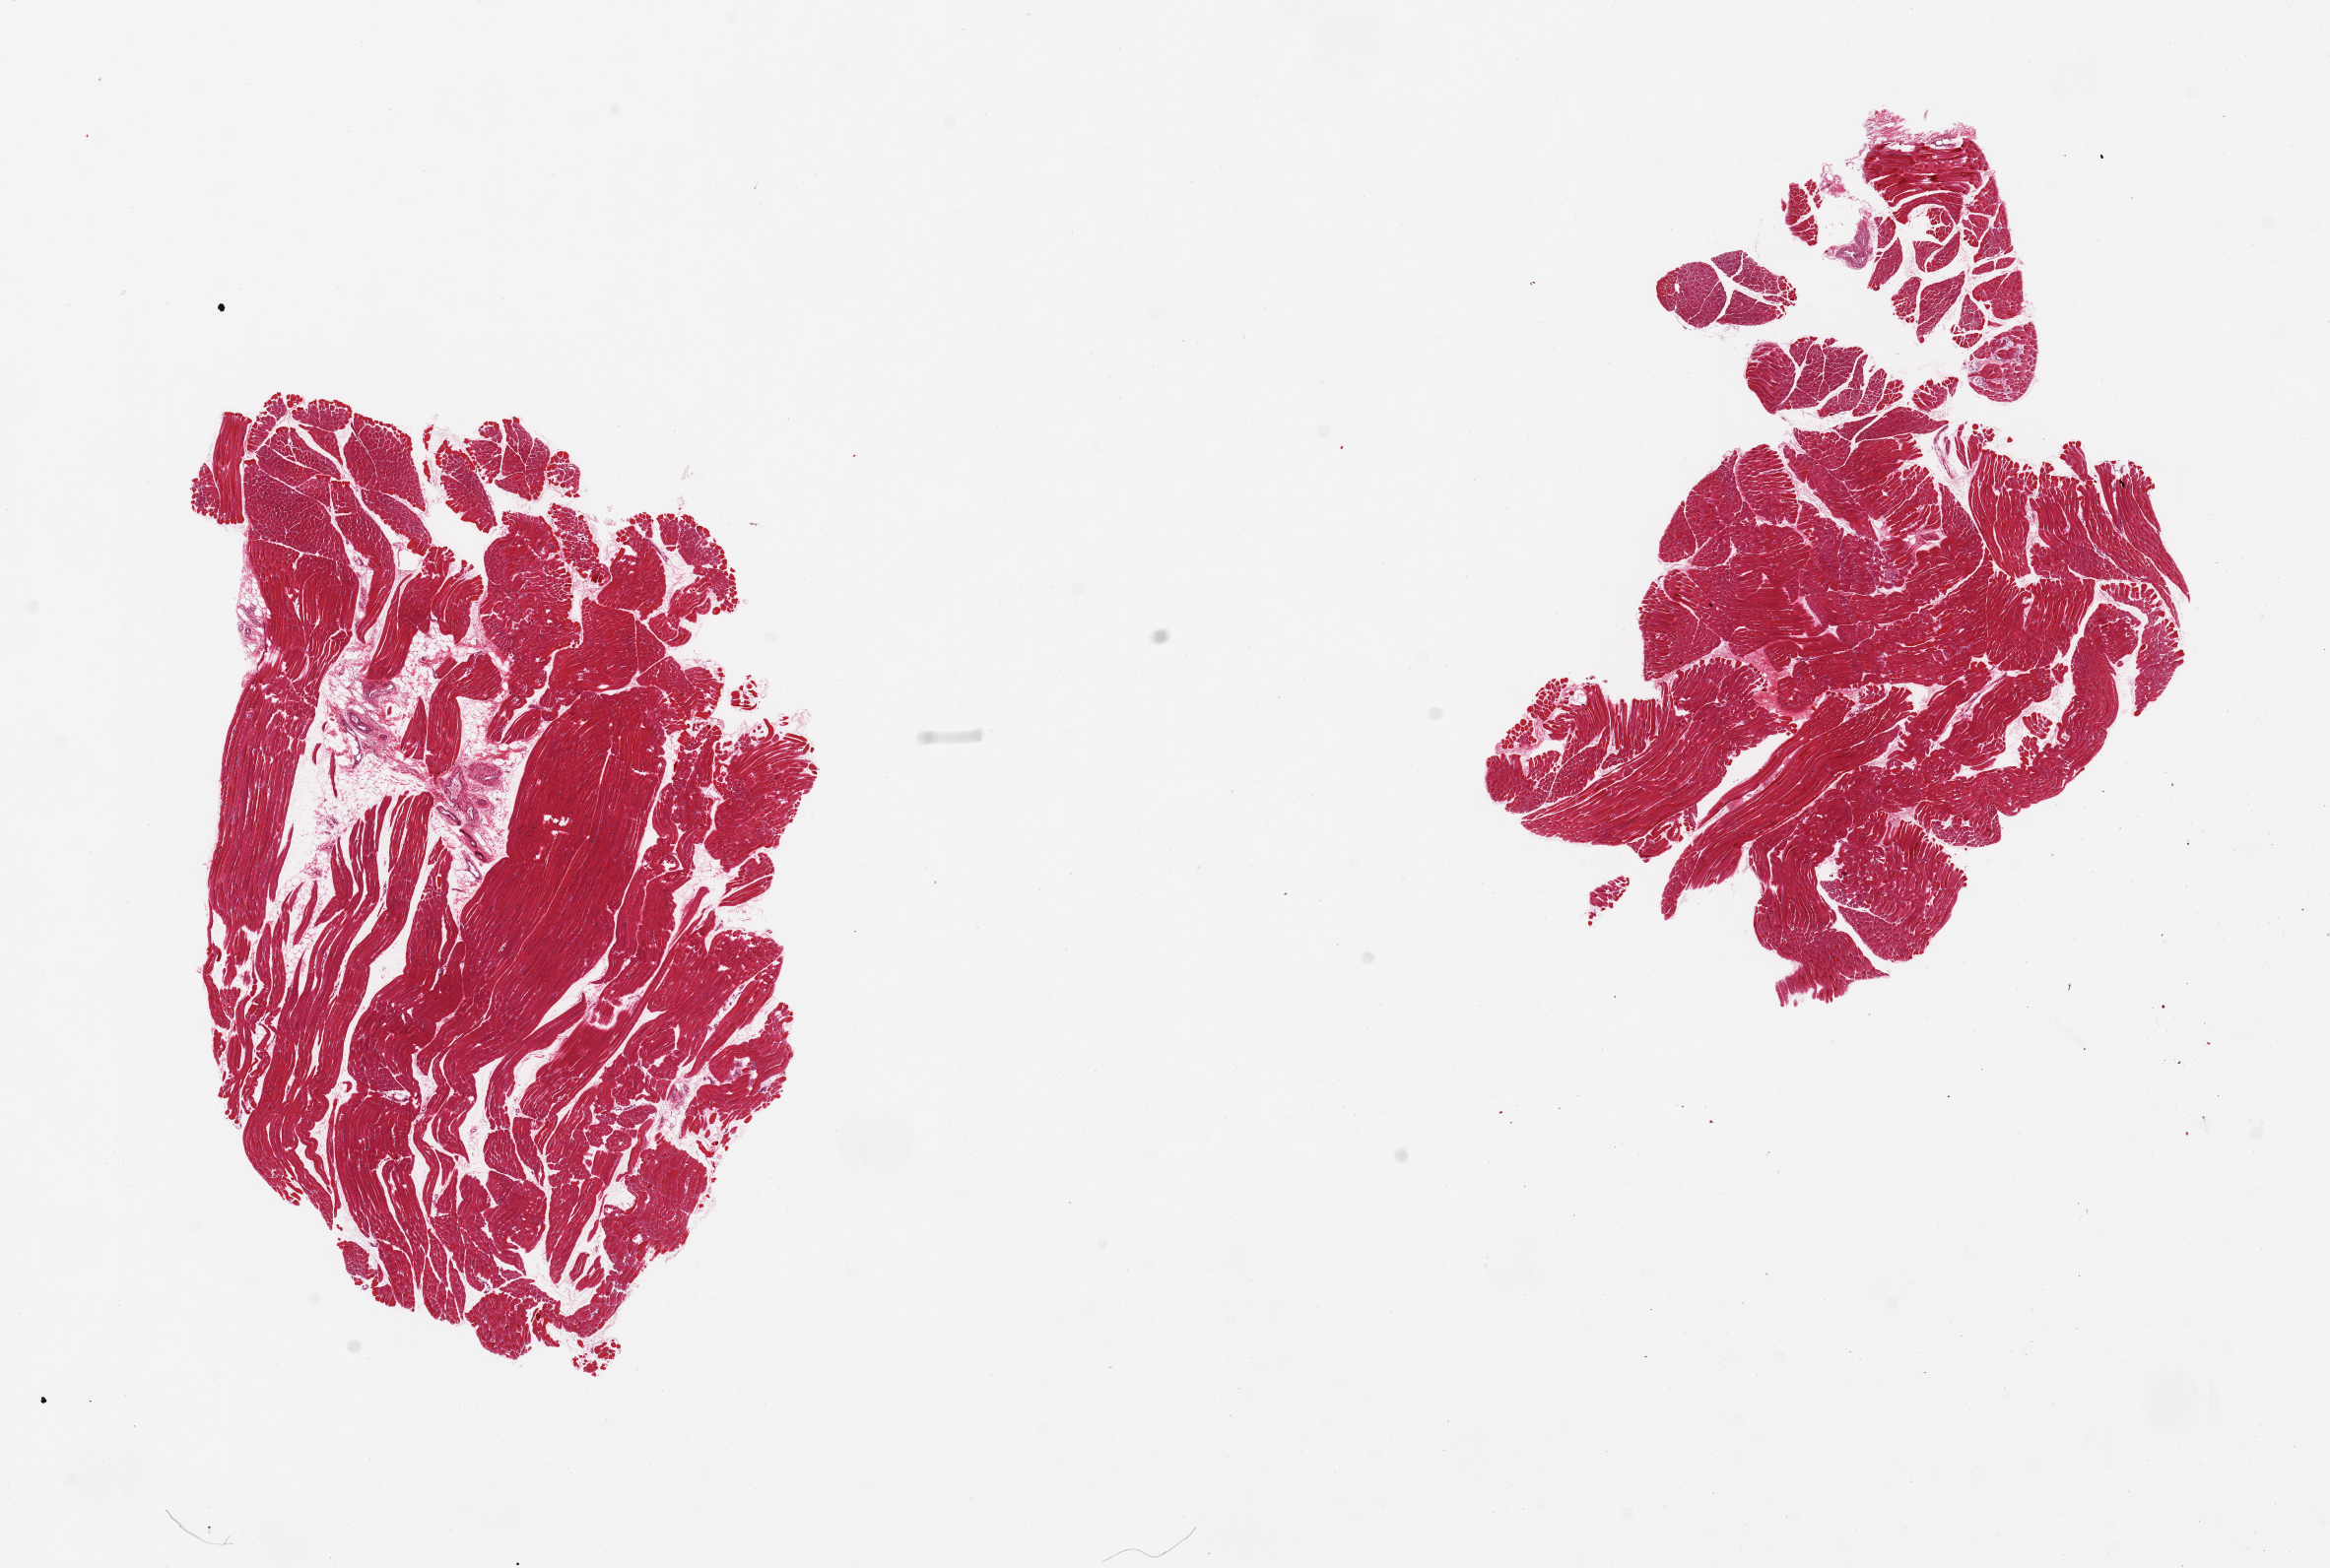
Digitized hematoxylin and eosin (H&E)-stained section — shown as a low-resolution overview of the whole scanned area (about 18.7 x 12.6 mm). PAXgene-fixed paraffin-embedded (PFPE) section. Sampled site (target tissue): skeletal muscle. Donor tissue sample. Donor sex: female.
Pathologist's review note for this sample: 2 pieces, <10% internal fat.